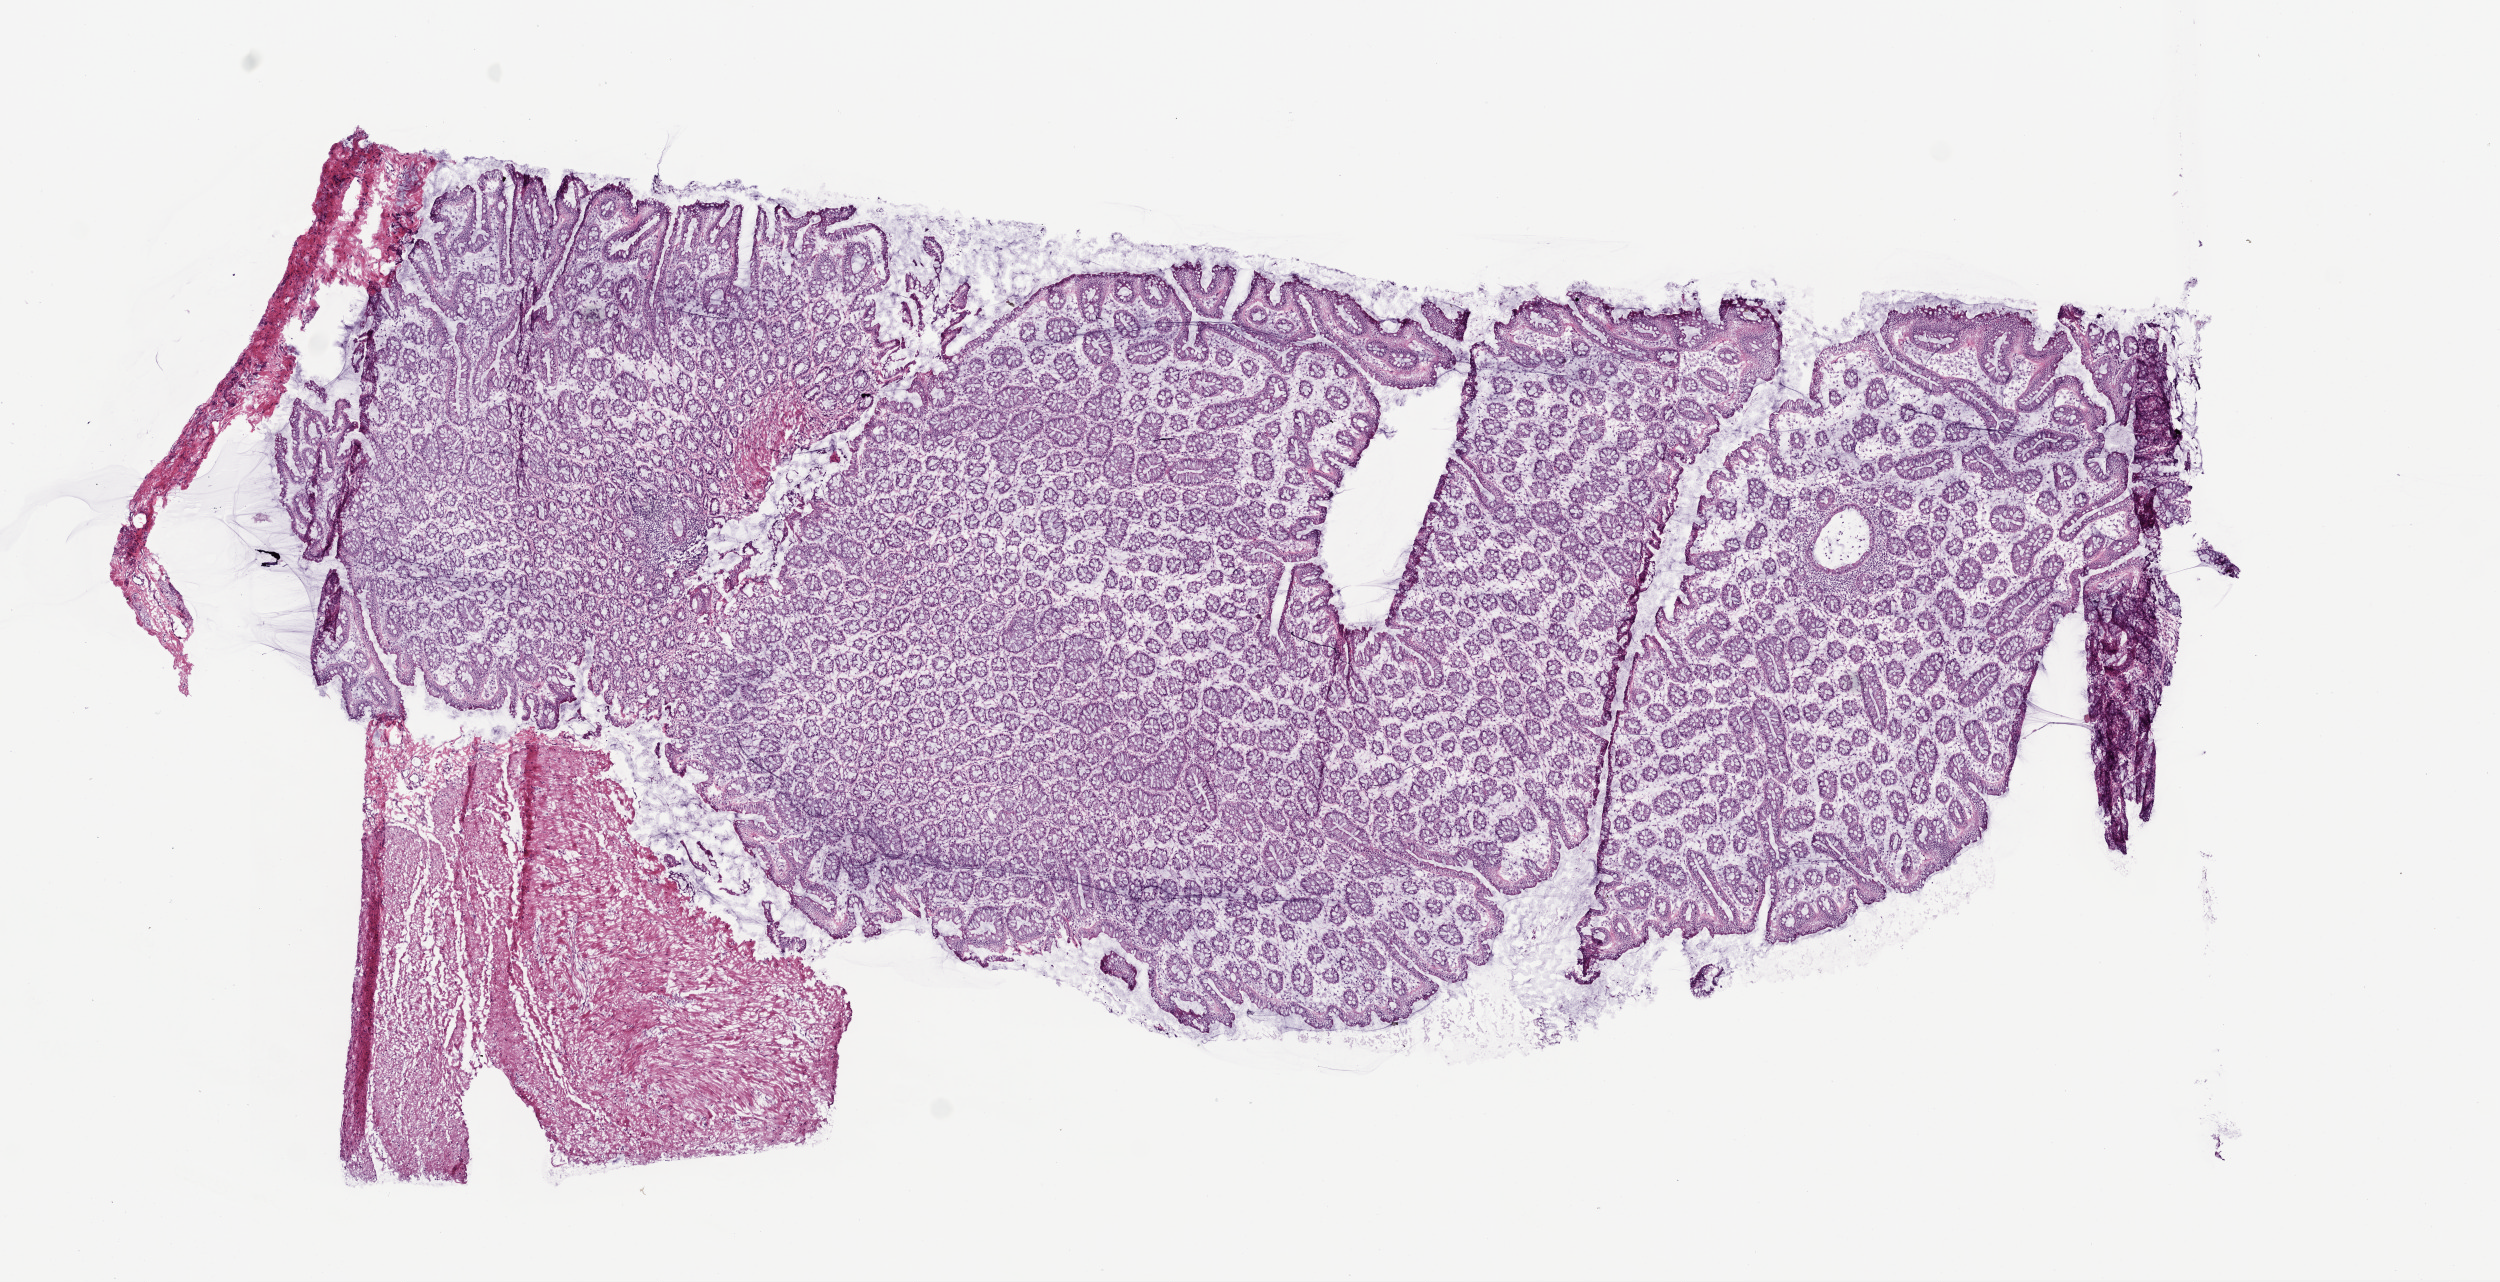
Hematoxylin and eosin (H&E) stained whole-slide image — a low-resolution overview of the entire scanned area, about 10.0 x 5.1 mm (from a 20x scan). Frozen section from the top of the tissue portion. Sample: solid tissue normal (non-tumour tissue), colon. Female, age 80 years at initial diagnosis.
This section: solid tissue normal (non-tumour) sample from the same patient. Patient diagnosis: Adenocarcinoma, NOS.